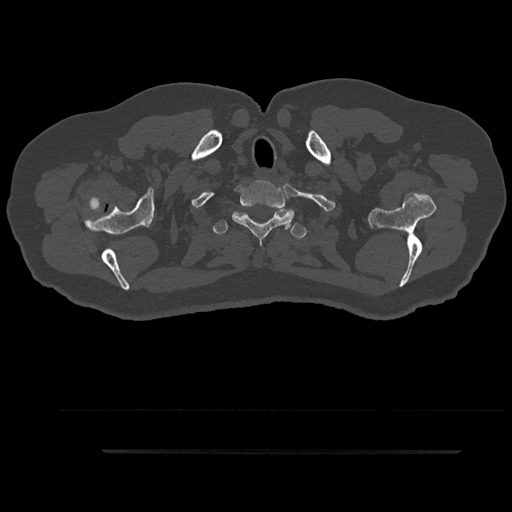
CT including the spine, one axial slice; position 789 of 797 along the scan axis; reconstruction kernel Br40s/3; bone window (W 1800 / L 400 HU); 0.5 mm slice thickness; 512 × 512 image matrix. Male patient, age 63 years. Case-level facts recorded for this patient, not image findings: primary cancer: renal; vertebrae with lytic lesions (as recorded): T8.
Structures marked on this image (semi-automatically segmented with operator editing):
- T1 vertebra: bounding box <232,185,294,244> (left, top, right, bottom; pixels)
- T2 vertebra: <212,209,306,239>